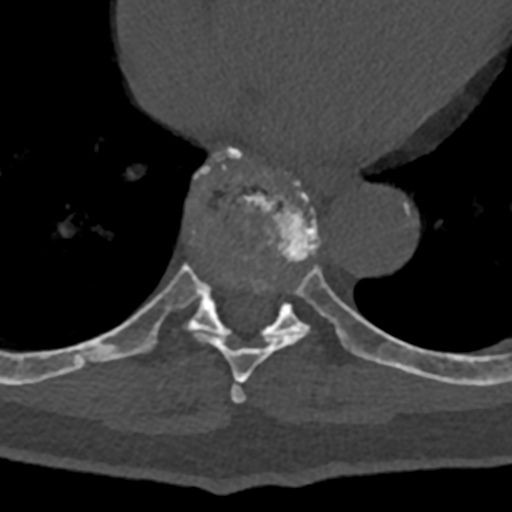
CT including the spine, one axial slice; slice 684 of 797 in the series (ordered by position); reconstruction kernel Br40s/3; bone window (W 1800 / L 400 HU); 0.5 mm slice thickness; 512 × 512 image matrix, field of view 160 × 160 mm. Male patient, age 74 years. From the clinical record (not read from this slice): primary cancer: renal.
Outlined on this slice (semi-automatically segmented with operator editing):
- T7 vertebra: bounding box [x1, y1, x2, y2] px = [231, 381, 246, 403]
- T8 vertebra: [70, 152, 363, 383]
- T9 vertebra: [87, 148, 432, 379]